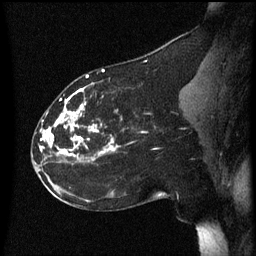
Breast MRI (dynamic contrast-enhanced), one sagittal slice. Position 27 of 60 along the scan axis. Dynamic contrast-enhanced series, image 2 of 3 at this slice position (ordered by acquisition). 1.5 T. TE 4.2 ms, TR 8.4 ms. 2.2 mm slice thickness. 256 × 256 image matrix. Patient: female, 35 years. From the clinical record (not read from this slice): setting: breast cancer imaged before/during neoadjuvant chemotherapy; receptor status: HER2-positive.
Structures marked on this image (semi-automatic segmentation, software-assisted and operator-edited):
- analysis volume of interest (the breast-tissue region the enhancement analysis was run in; not a lesion): bounding box (x1, y1, x2, y2) in pixels: (32, 72, 165, 173)
- tumour enhancement mask (voxels above the 70 % enhancement threshold inside the analysis volume of interest): (40, 72, 117, 161)